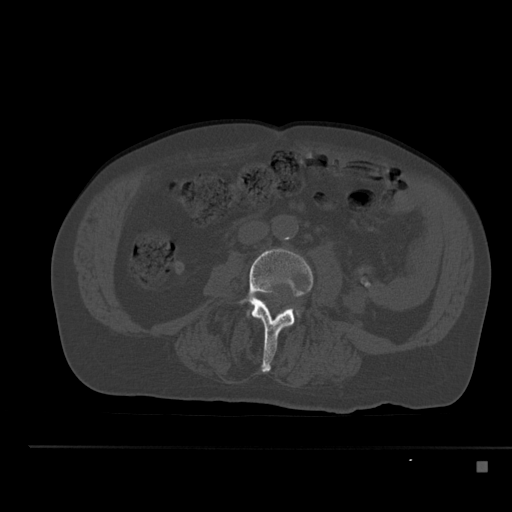
CT including the spine, one axial slice; slice 160 of 517 in the series (ordered by position); reconstruction kernel Br40s; 120 kVp; bone window (W 1800 / L 400 HU); 1.5 mm slice thickness; 512 × 512 image matrix, field of view 408 × 408 mm. Patient: male, 70 years. Case-level facts recorded for this patient, not image findings: primary cancer: renal; vertebrae with lytic lesions (as recorded): T4, T6, T10, T12, L3, L4, L5.
Annotated regions visible in this slice (semi-automatic segmentation, software-assisted and operator-edited):
- L3 vertebra: box from (x=238, y=249) to (x=313, y=372) px